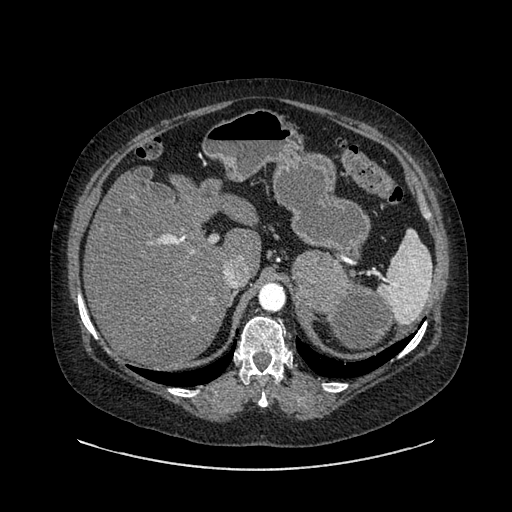
Contrast-enhanced abdominal CT, one axial slice. Position 611 of 769 along the scan axis. 120 kVp. Intravenous contrast given. Soft-tissue window (W 400 / L 40 HU). 0.62 mm slice thickness. 512 × 512 image matrix. Patient: female, 61 years. Case-level facts recorded for this patient, not image findings: diagnosis: adrenocortical carcinoma; tumour side: left adrenal; tumour size at pathology: 13 cm.
Structures marked on this image (semi-automatically segmented with operator editing):
- mass: bounding box (x1, y1, x2, y2) in pixels: (293, 235, 512, 349)